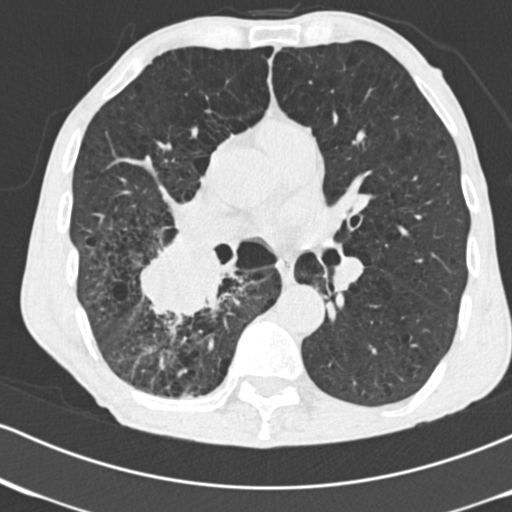
Chest CT (low-dose screening protocol), one axial image. Second screening round (one year after baseline). Lung window (W 1500 / L -600 HU). 2 mm slice thickness. Slice 95 of 182 in the series. 512 × 512 image matrix, field of view 316 × 316 mm. Male, age 64 years at enrolment. Current smoker at enrolment.
Lesion marked by an expert reader, box from (x=129, y=228) to (x=240, y=331) px. Reader record for this screening exam (exam-level; its link to the box is not recorded): non-calcified nodule or mass ≥4 mm, 52 × 37 mm, spiculated (stellate) margins, soft tissue attenuation, pre-existing on the prior screen: no.